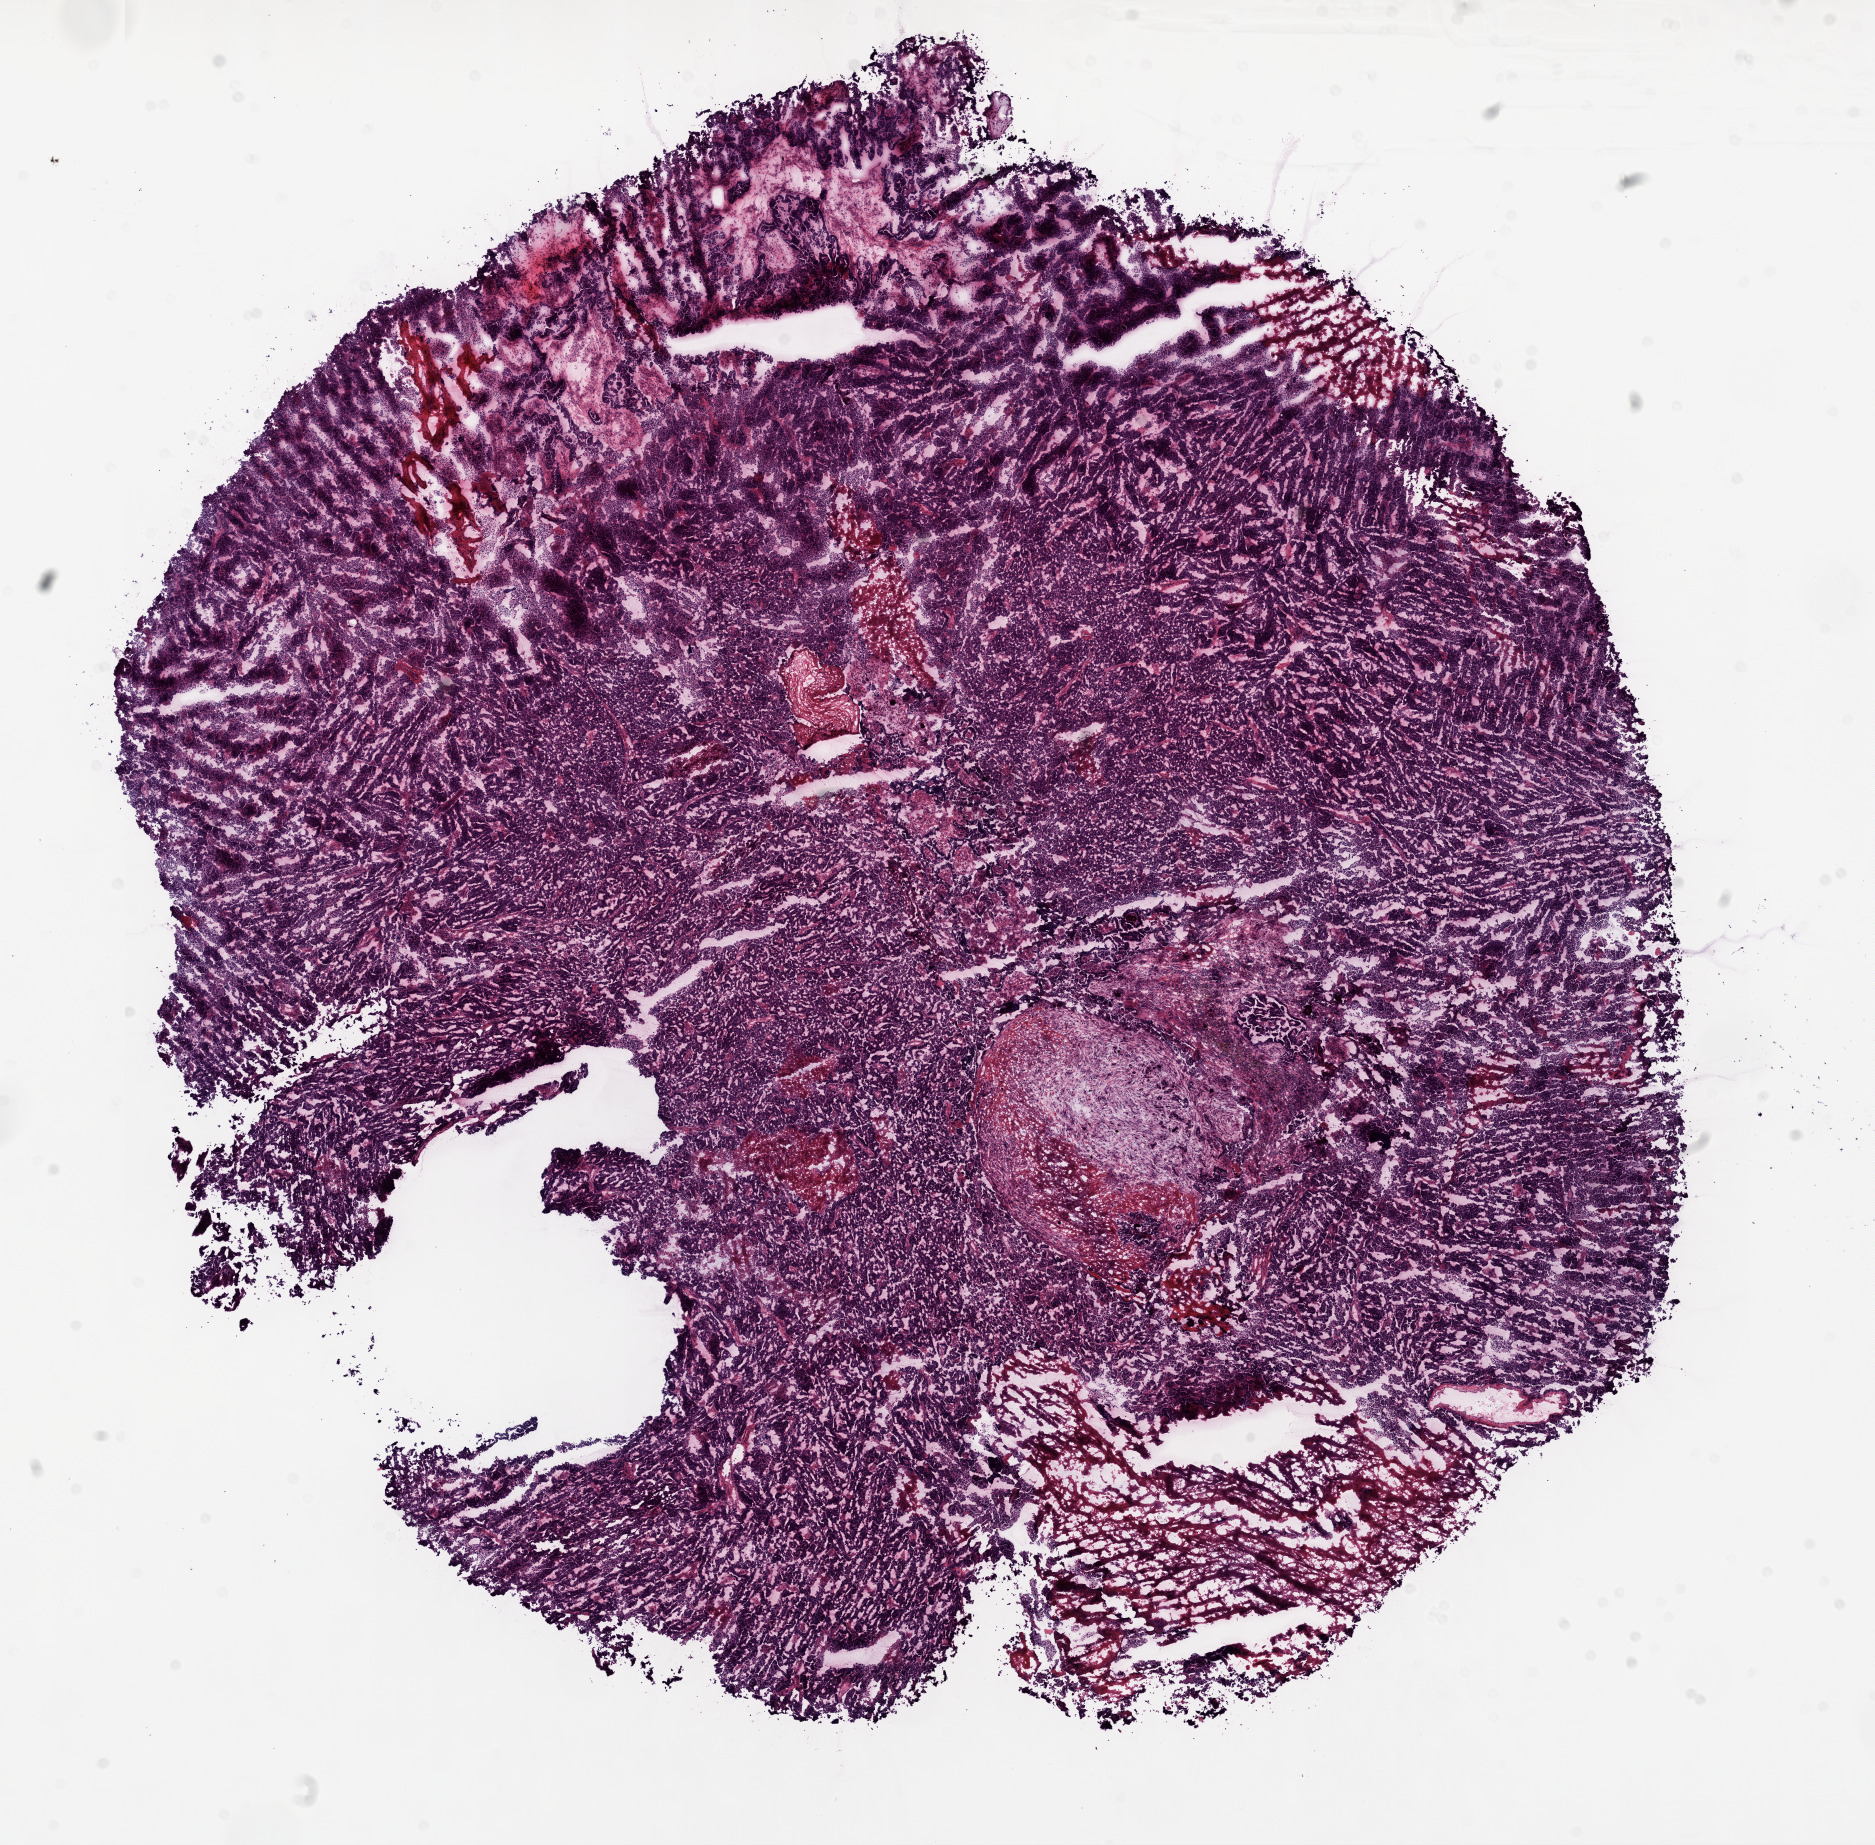
Hematoxylin and eosin (H&E) stained whole-slide image — a low-resolution overview of the entire scanned area, about 15.0 x 14.8 mm (slide scanned at 20x). Frozen section from the top of the tissue portion. Sample: primary tumour, ovary. Female patient; age at initial diagnosis 47 years. Histologic grade: G3 (poorly differentiated). Composition of this section per pathologist review: tumour cells 80%, tumour nuclei 95%, normal cells 0%, stromal cells 5%, necrosis 15%.
FIGO stage: IIIC. Histologic diagnosis: Serous cystadenocarcinoma, NOS.